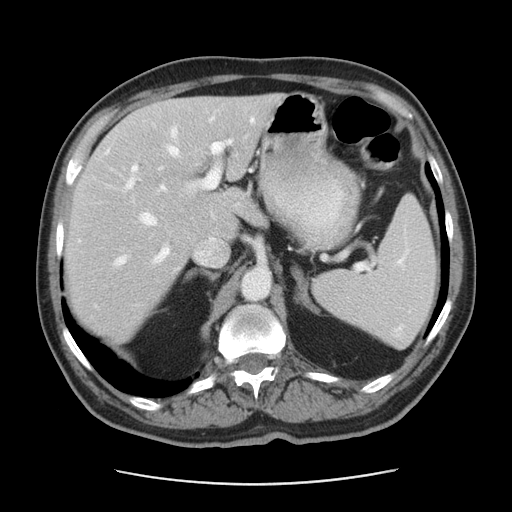
Contrast-enhanced abdominal CT, one axial slice; slice 29 of 42 in the series (ordered by position); reconstruction kernel STANDARD; 120 kVp; intravenous contrast given; soft-tissue window (W 400 / L 40 HU); 5 mm slice thickness; 512 × 512 image matrix, field of view 370 × 370 mm. Male patient, age 73 years. Case-level facts recorded for this patient, not image findings: diagnosis: colorectal cancer liver metastases, imaged before liver resection.
Structures marked on this image (outlined manually by an expert reader):
- hepatic veins: bounding box <113,118,254,267> (left, top, right, bottom; pixels)
- liver: <67,97,275,340>
- planned liver remnant (the part of the liver to remain after resection): <113,97,275,237>
- portal vein (with intrahepatic branches): <127,140,231,265>